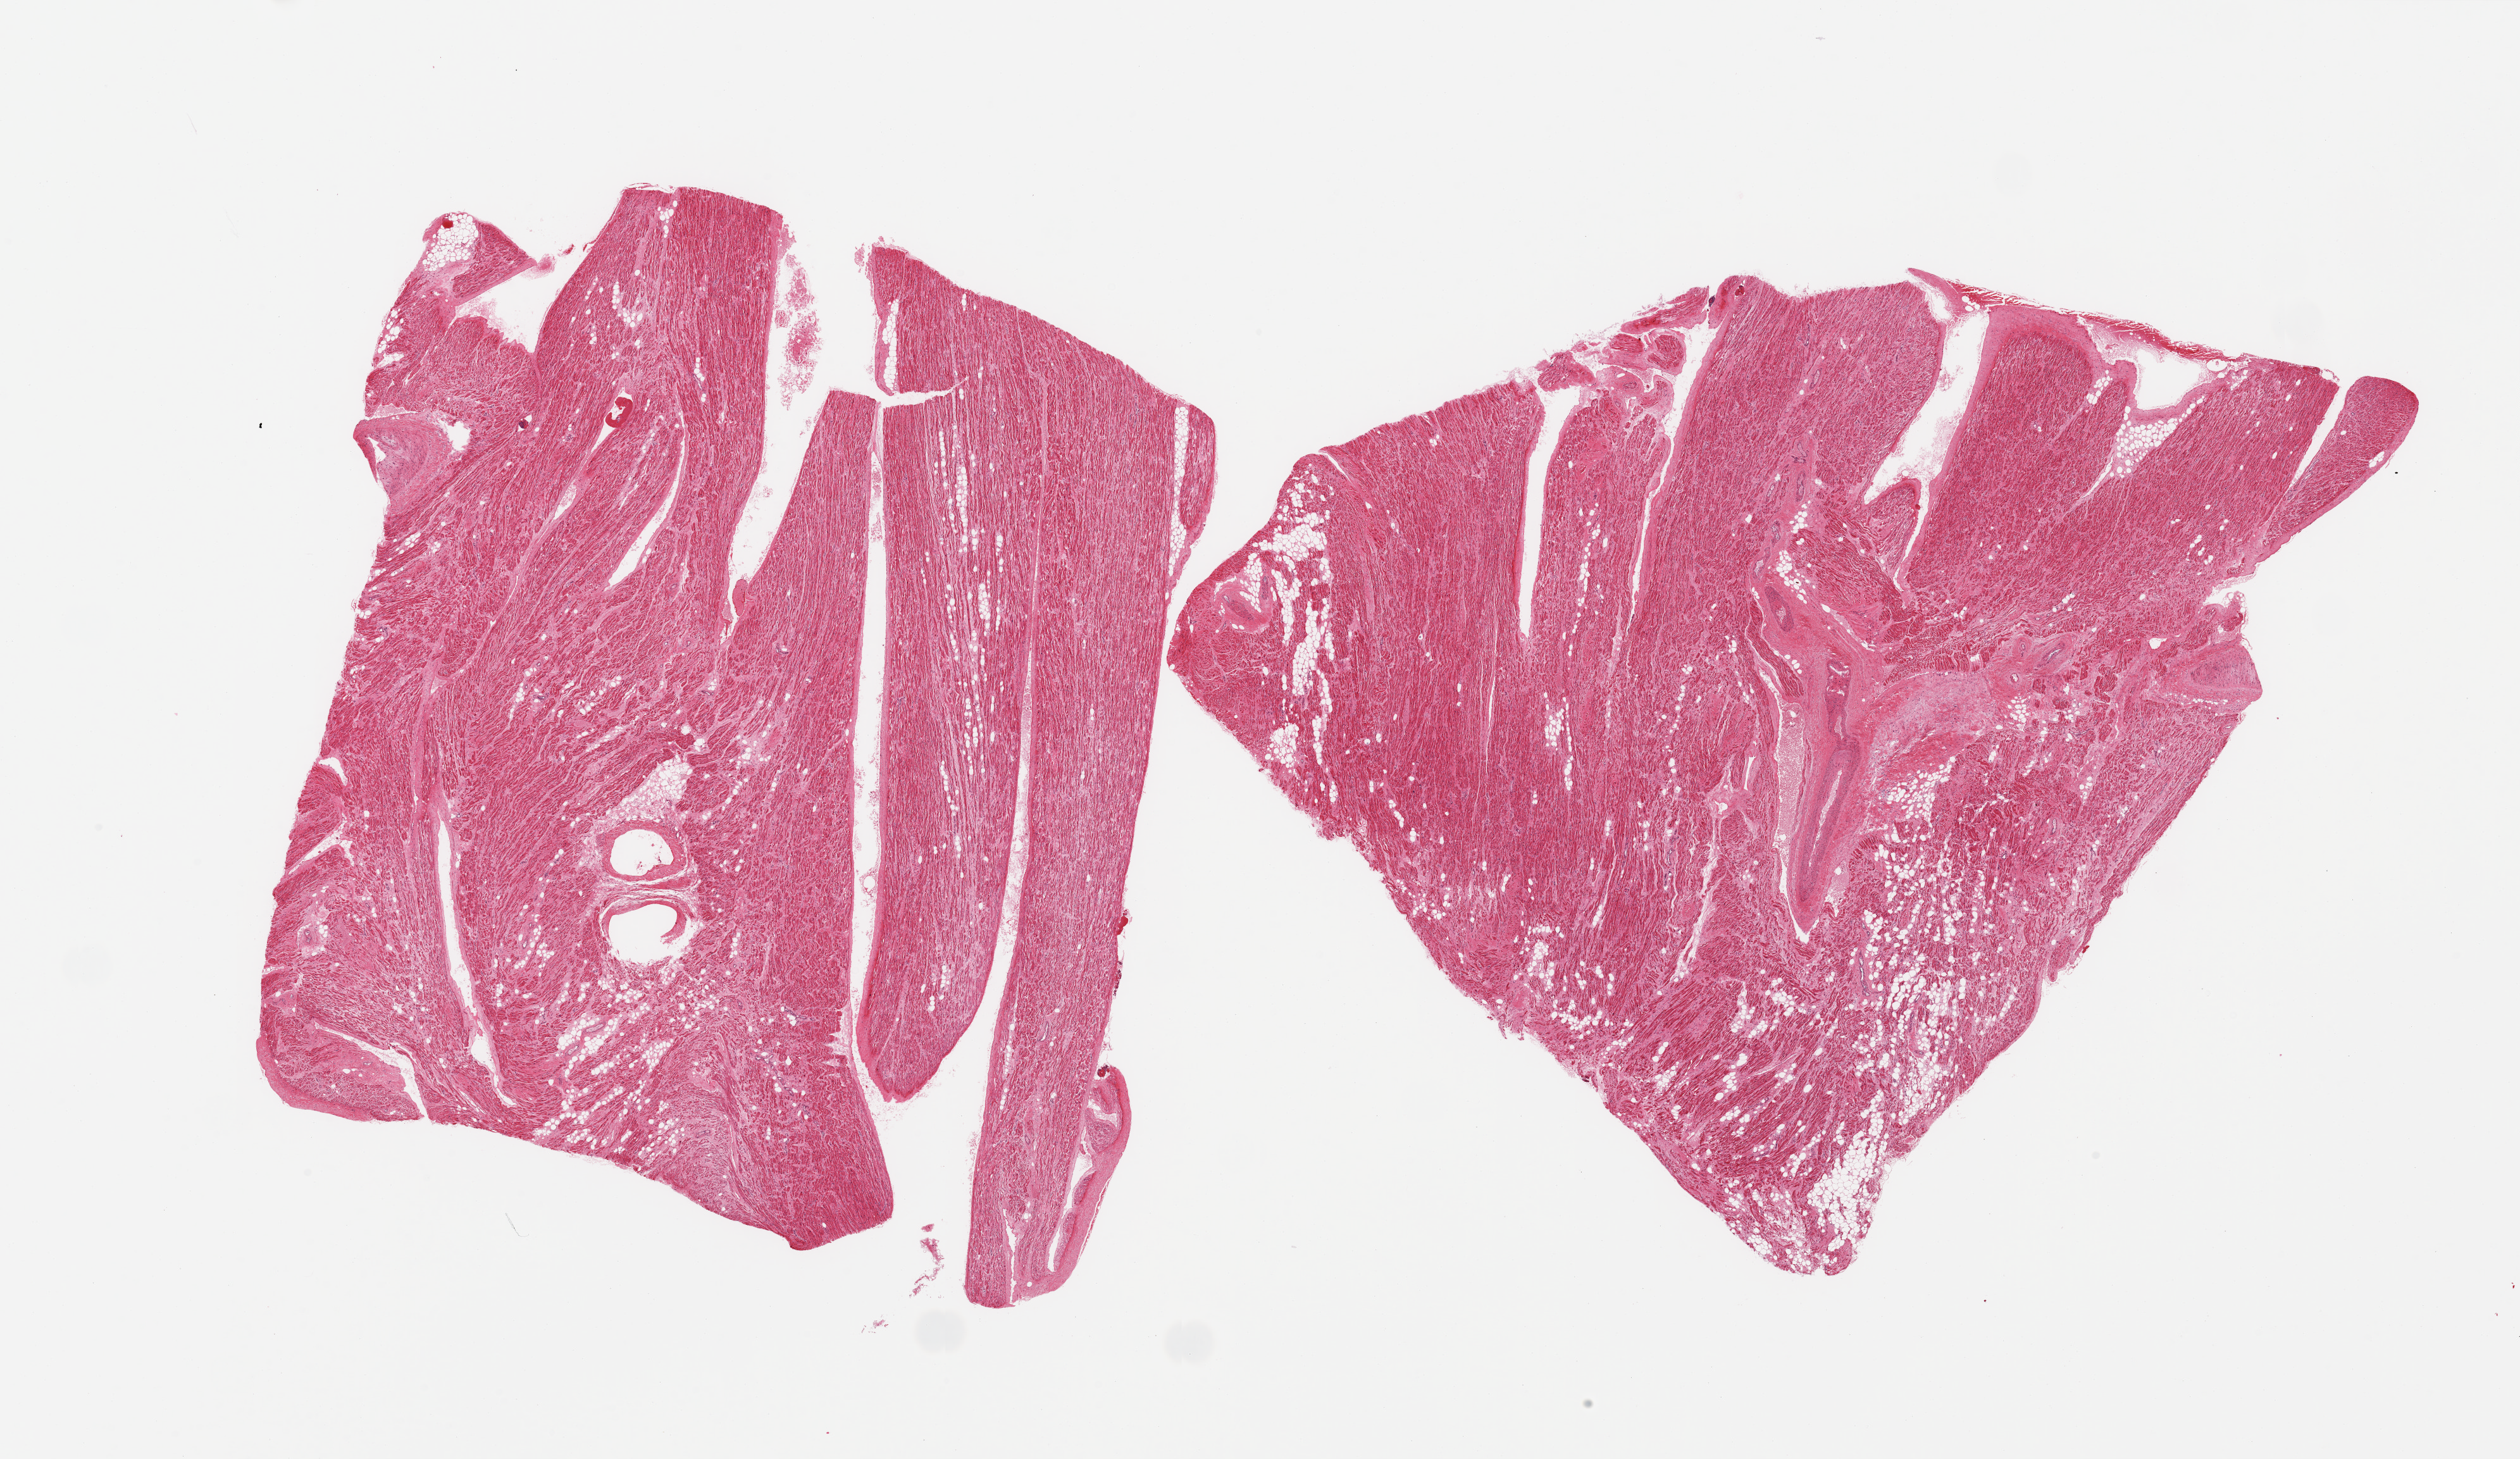
Whole-slide image, hematoxylin and eosin (H&E) stain, low-resolution overview of the scanned area, about 31.5 x 18.2 mm (slide scanned at 20x); PAXgene-fixed paraffin-embedded (PFPE) section; sampled site (target tissue): auricular appendage; donor tissue sample.
Reviewer comment on this tissue sample: 2 pieces, no abnormalities.